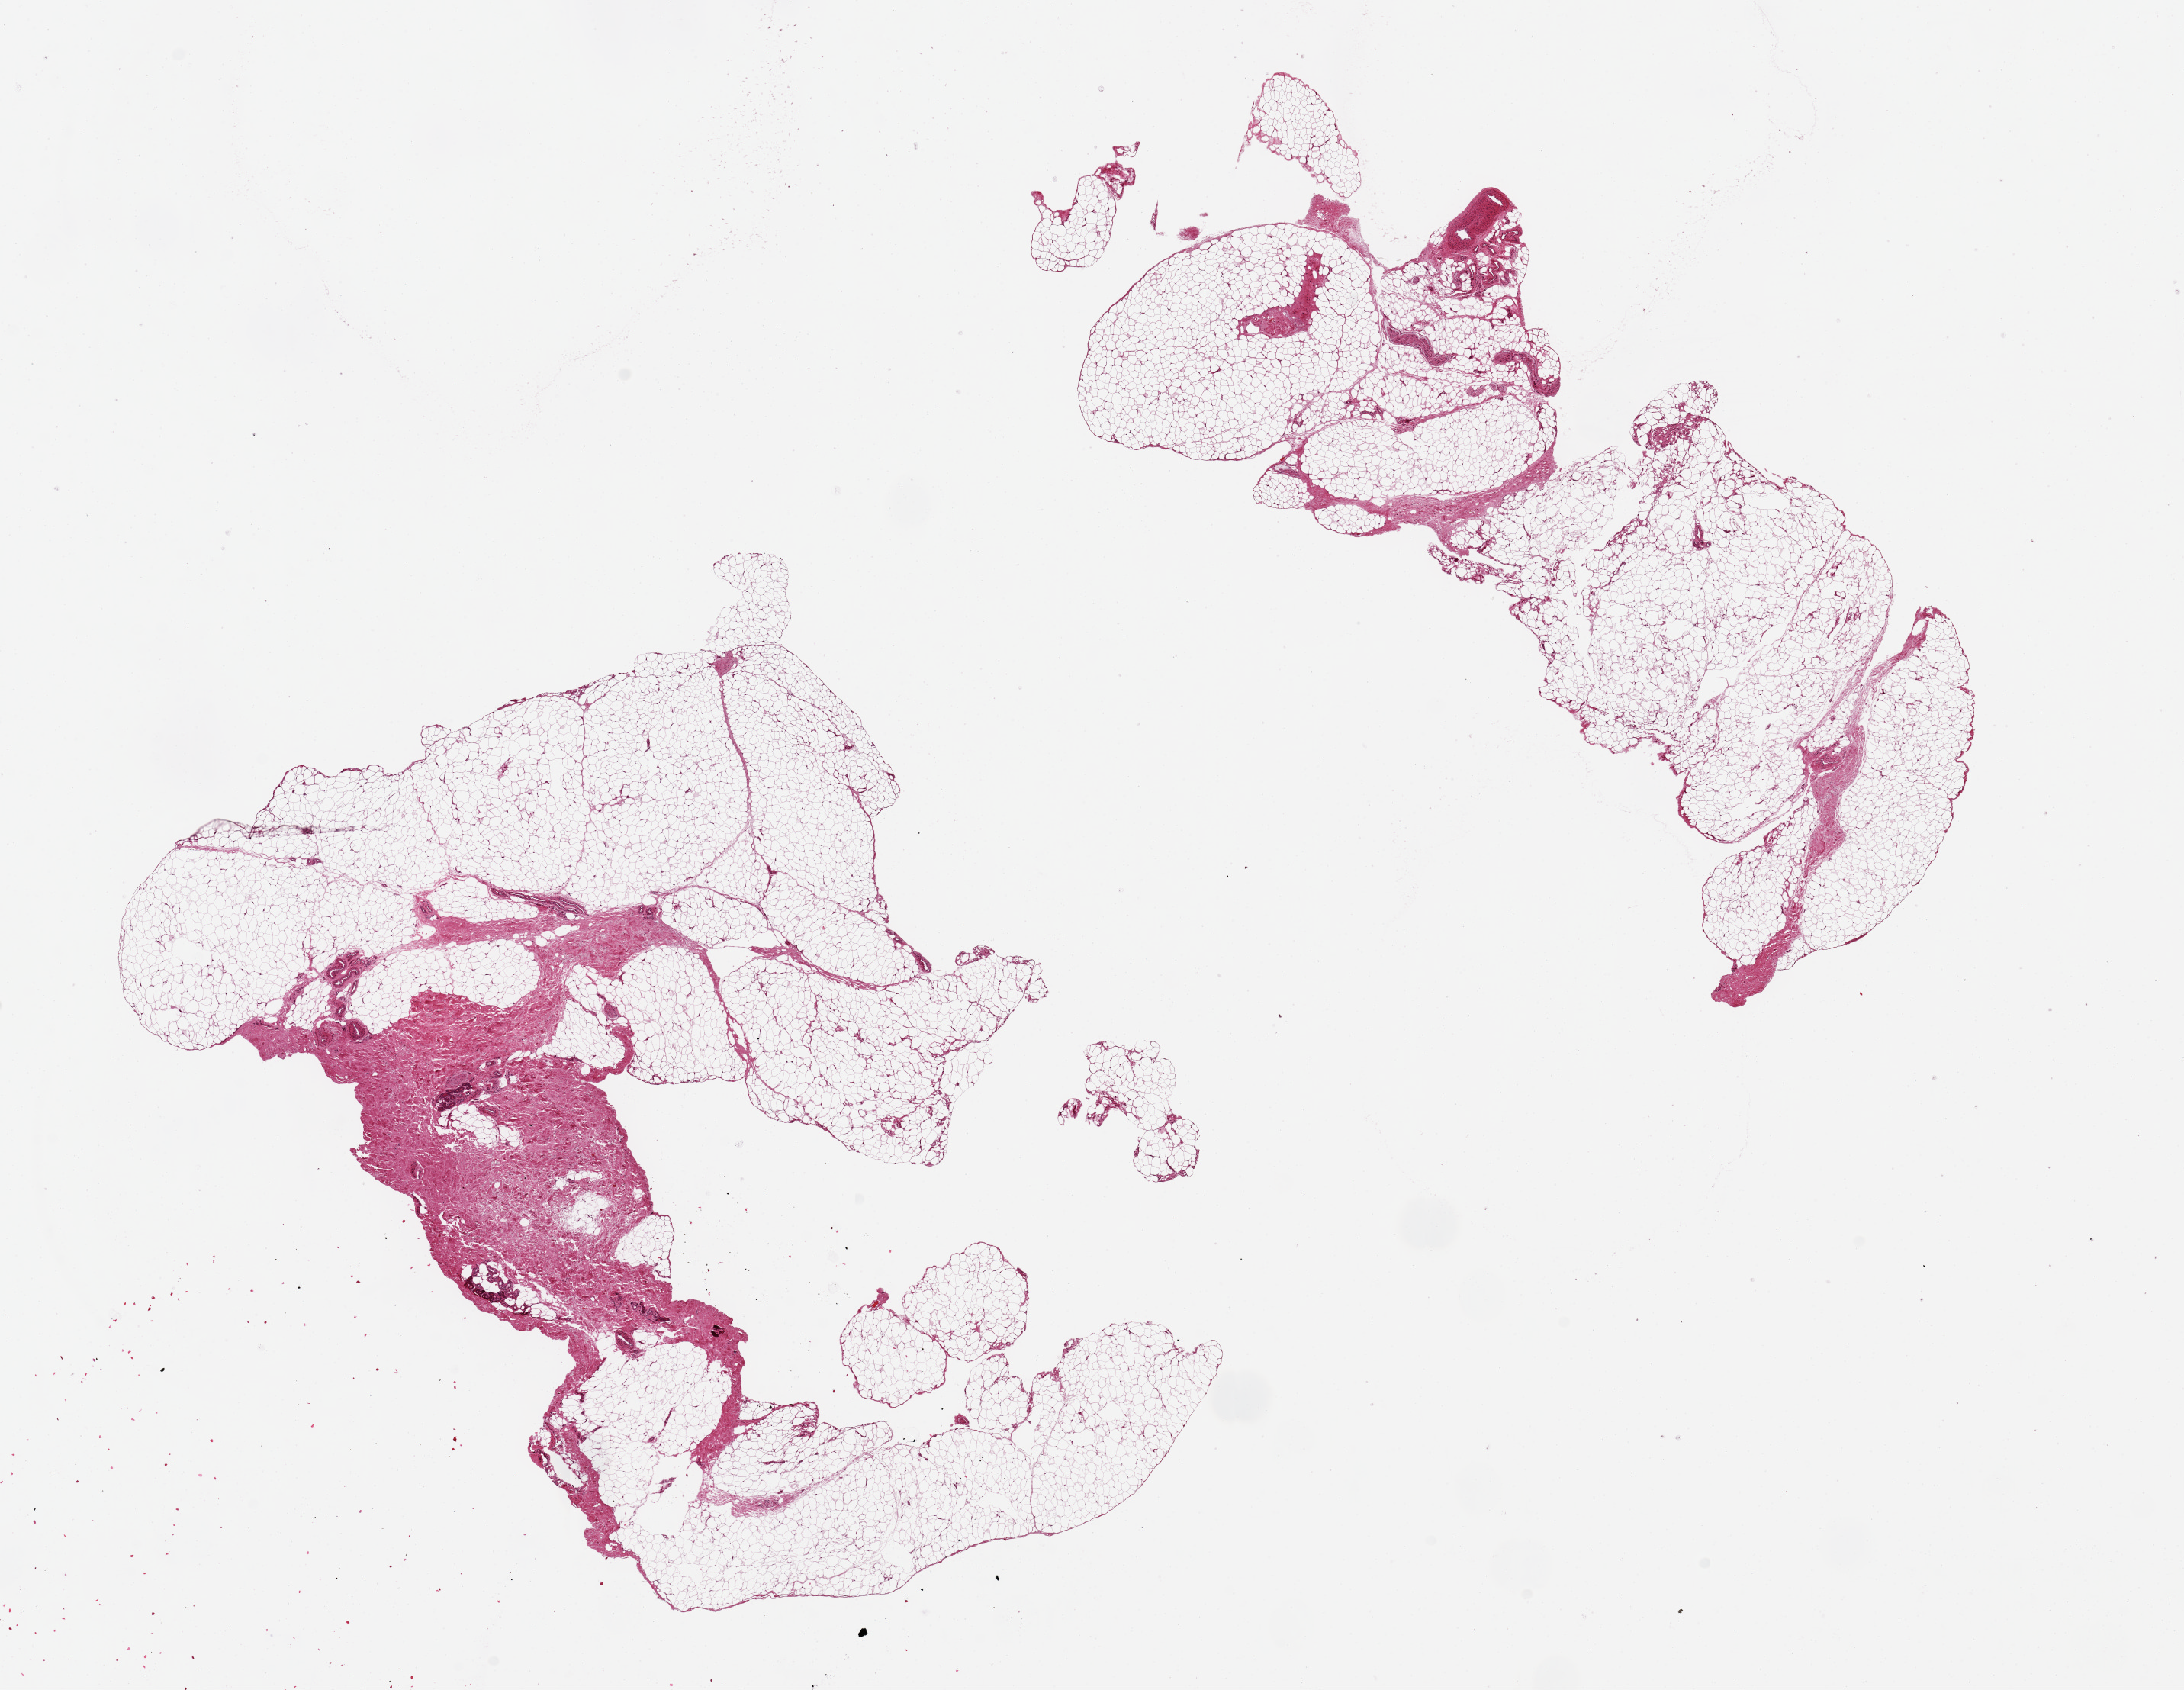
Digitized H&E-stained section, whole scanned area (about 22.6 x 17.5 mm, slide scanned at 20x) shown as a low-resolution overview; PAXgene-fixed paraffin-embedded (PFPE) section; target tissue: adipose tissue; donor tissue sample. Donor sex: male.
Review note (as recorded): 2 pieces. 10x8 & 12x5mm; 1 with 20% fibrous tissue.